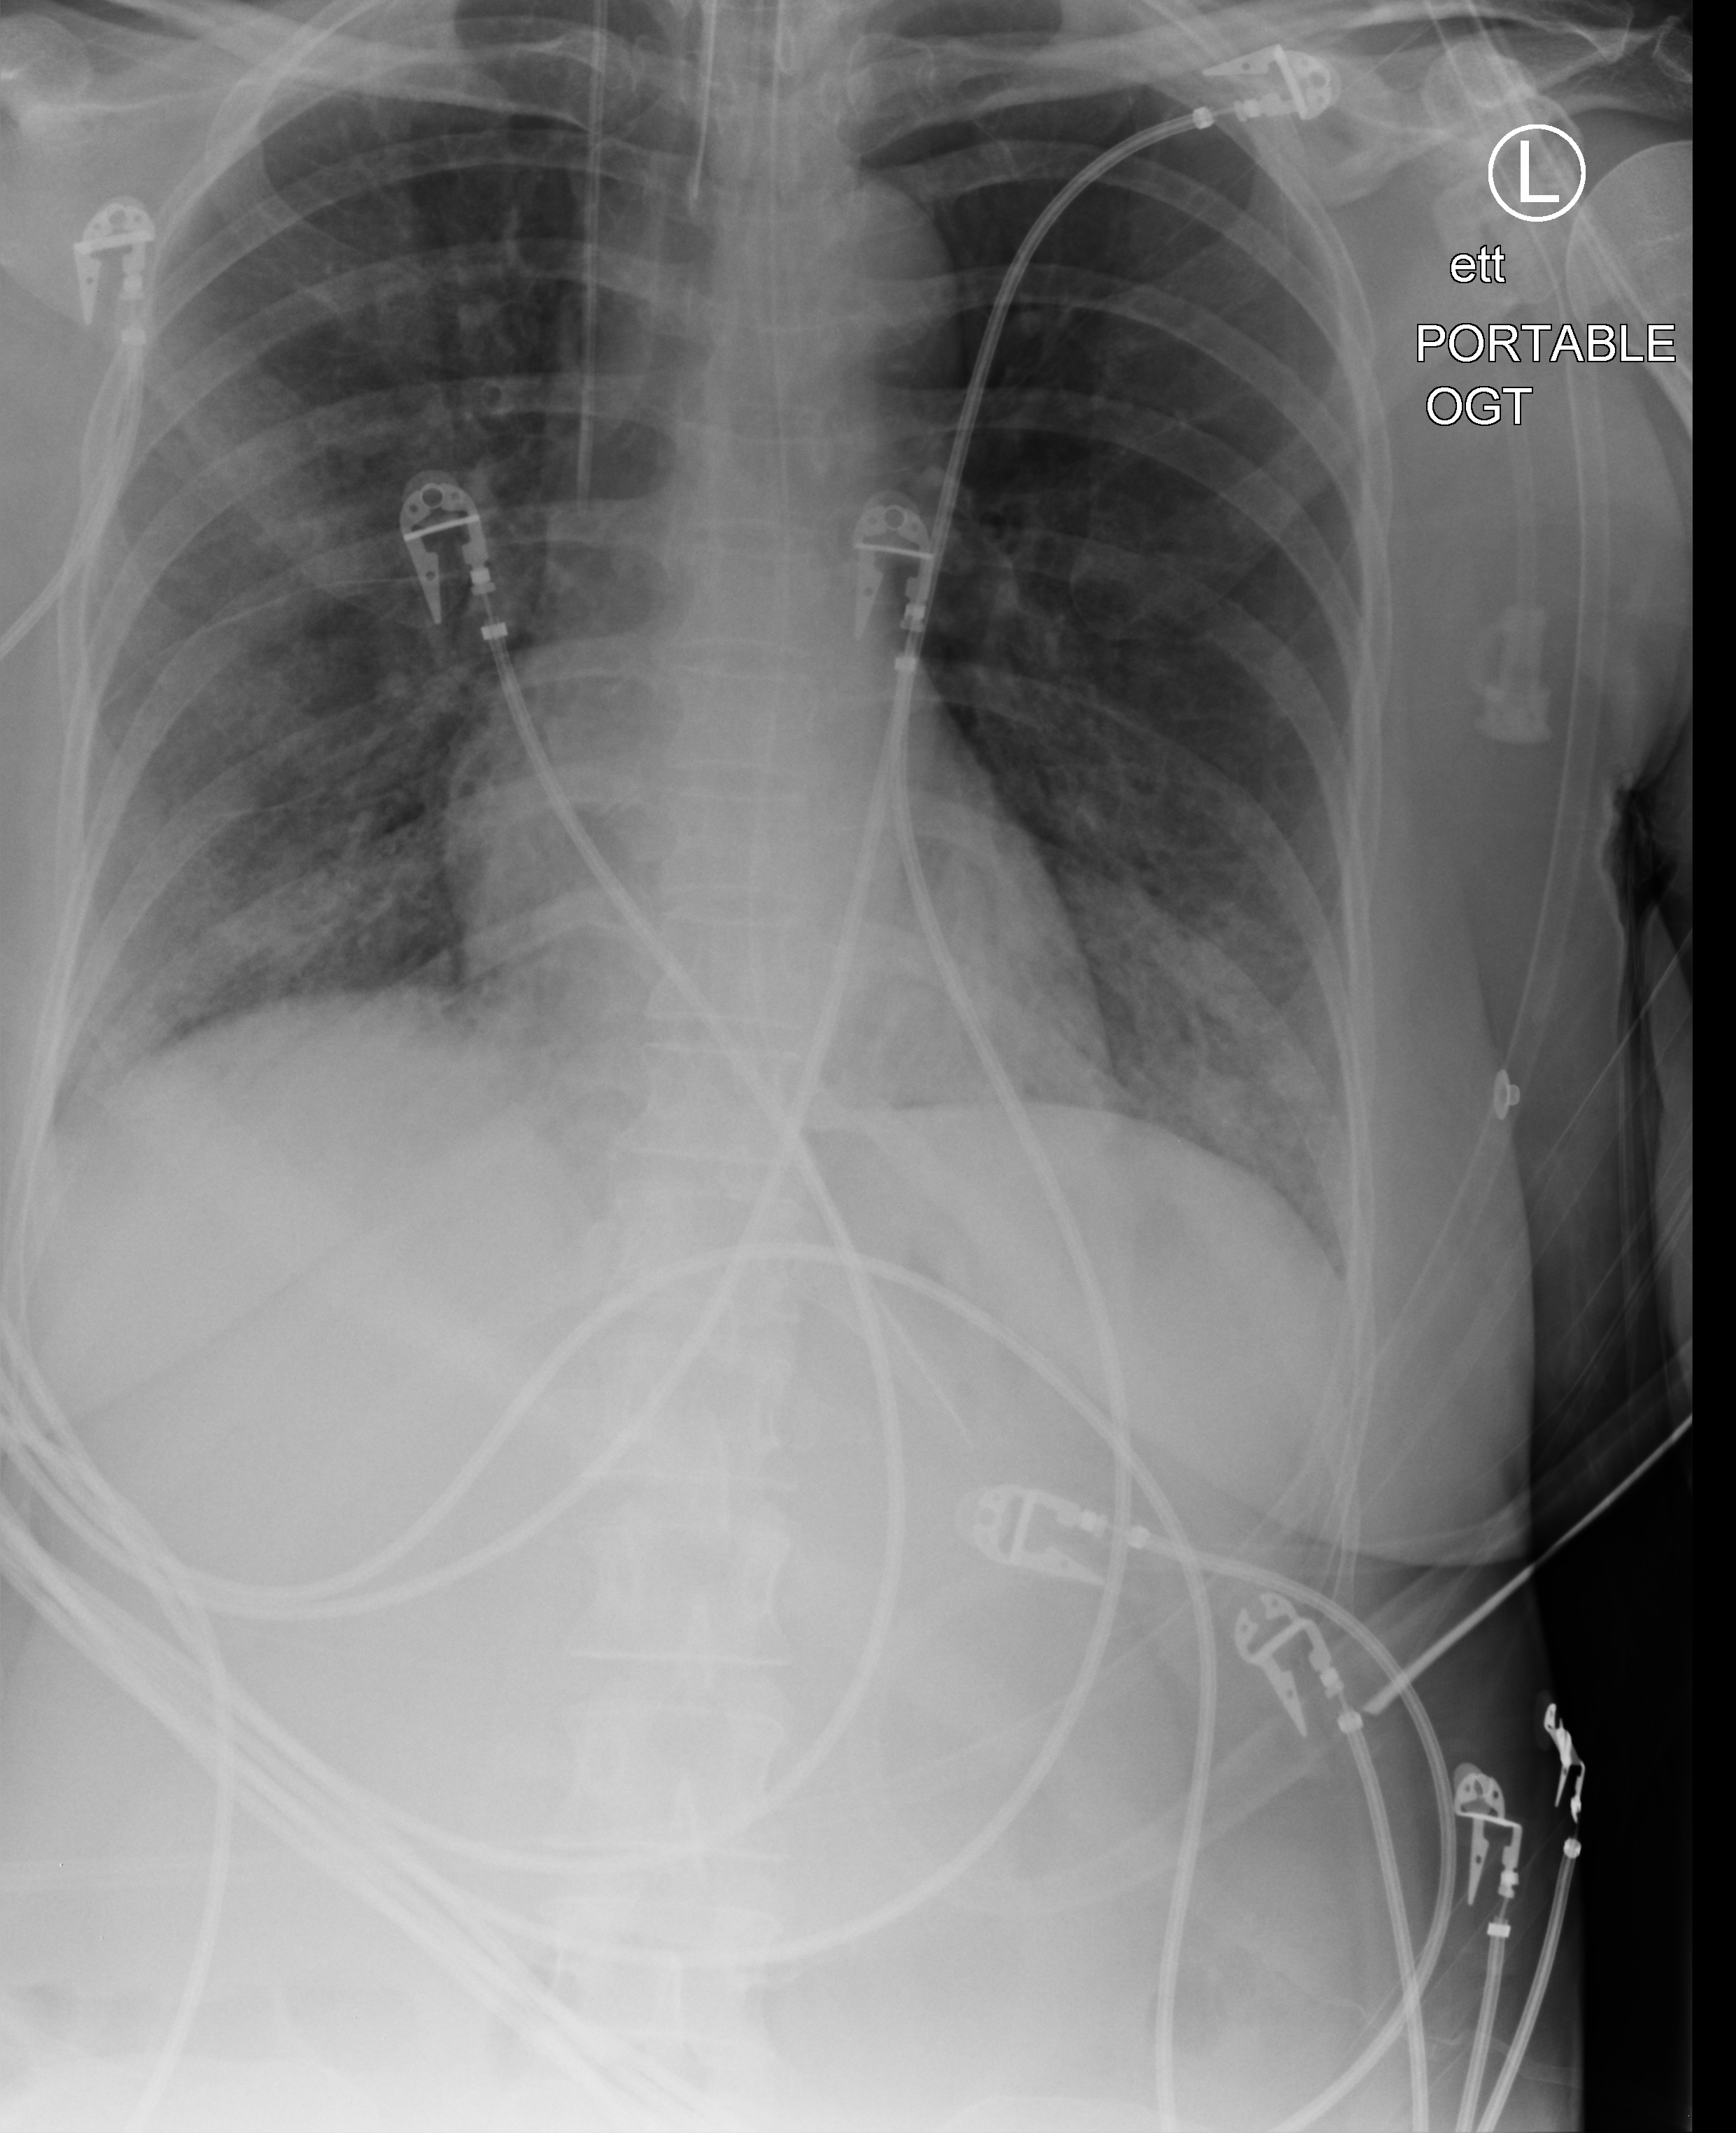
Chest X-ray (portable); anteroposterior (AP) projection. Patient hospitalised with COVID-19; female, aged 18–59 years.
Admission-level facts for this patient (not findings on this image; timing relative to this image not recorded): chronic kidney disease (admission record): no.